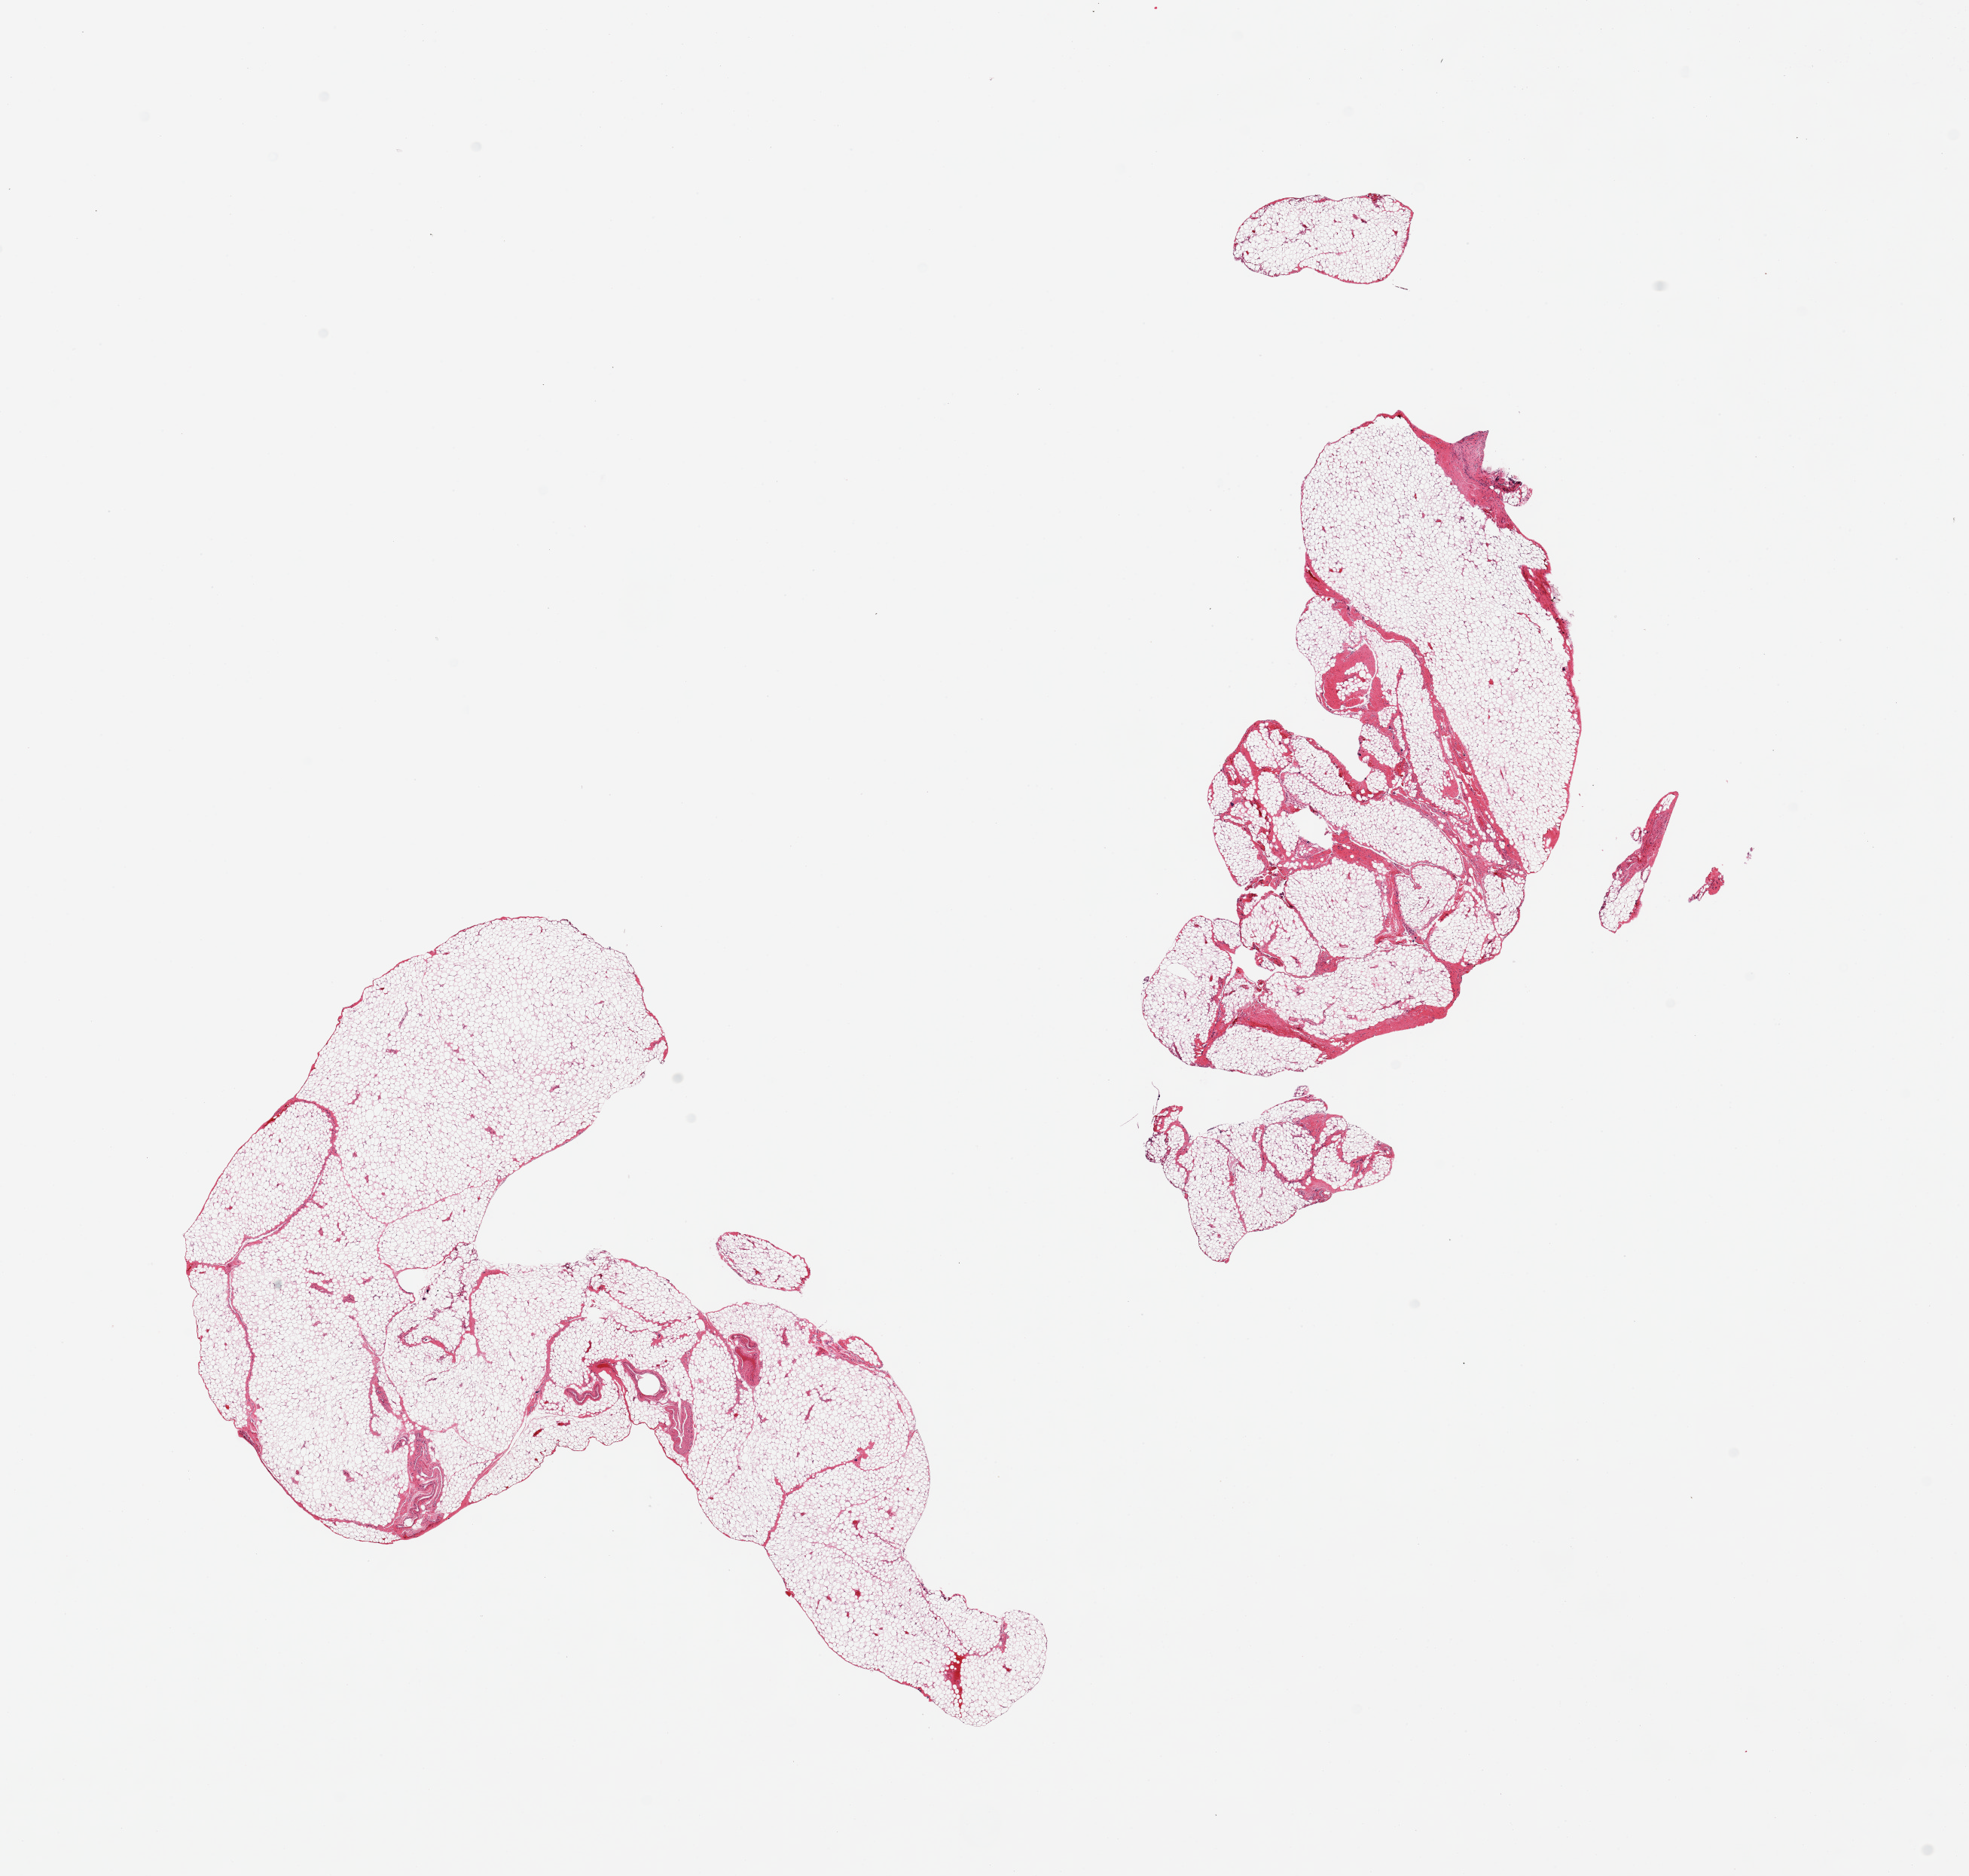
Digitized haematoxylin and eosin-stained section, brightfield — low-resolution overview of the scanned area, about 20.7 x 19.7 mm (slide scanned at 20x). PAXgene-fixed, paraffin-embedded tissue. Target tissue: omentum. Tissue donor sample. Donor sex: male.
Pathologist's review note for this sample: 2 pieces.